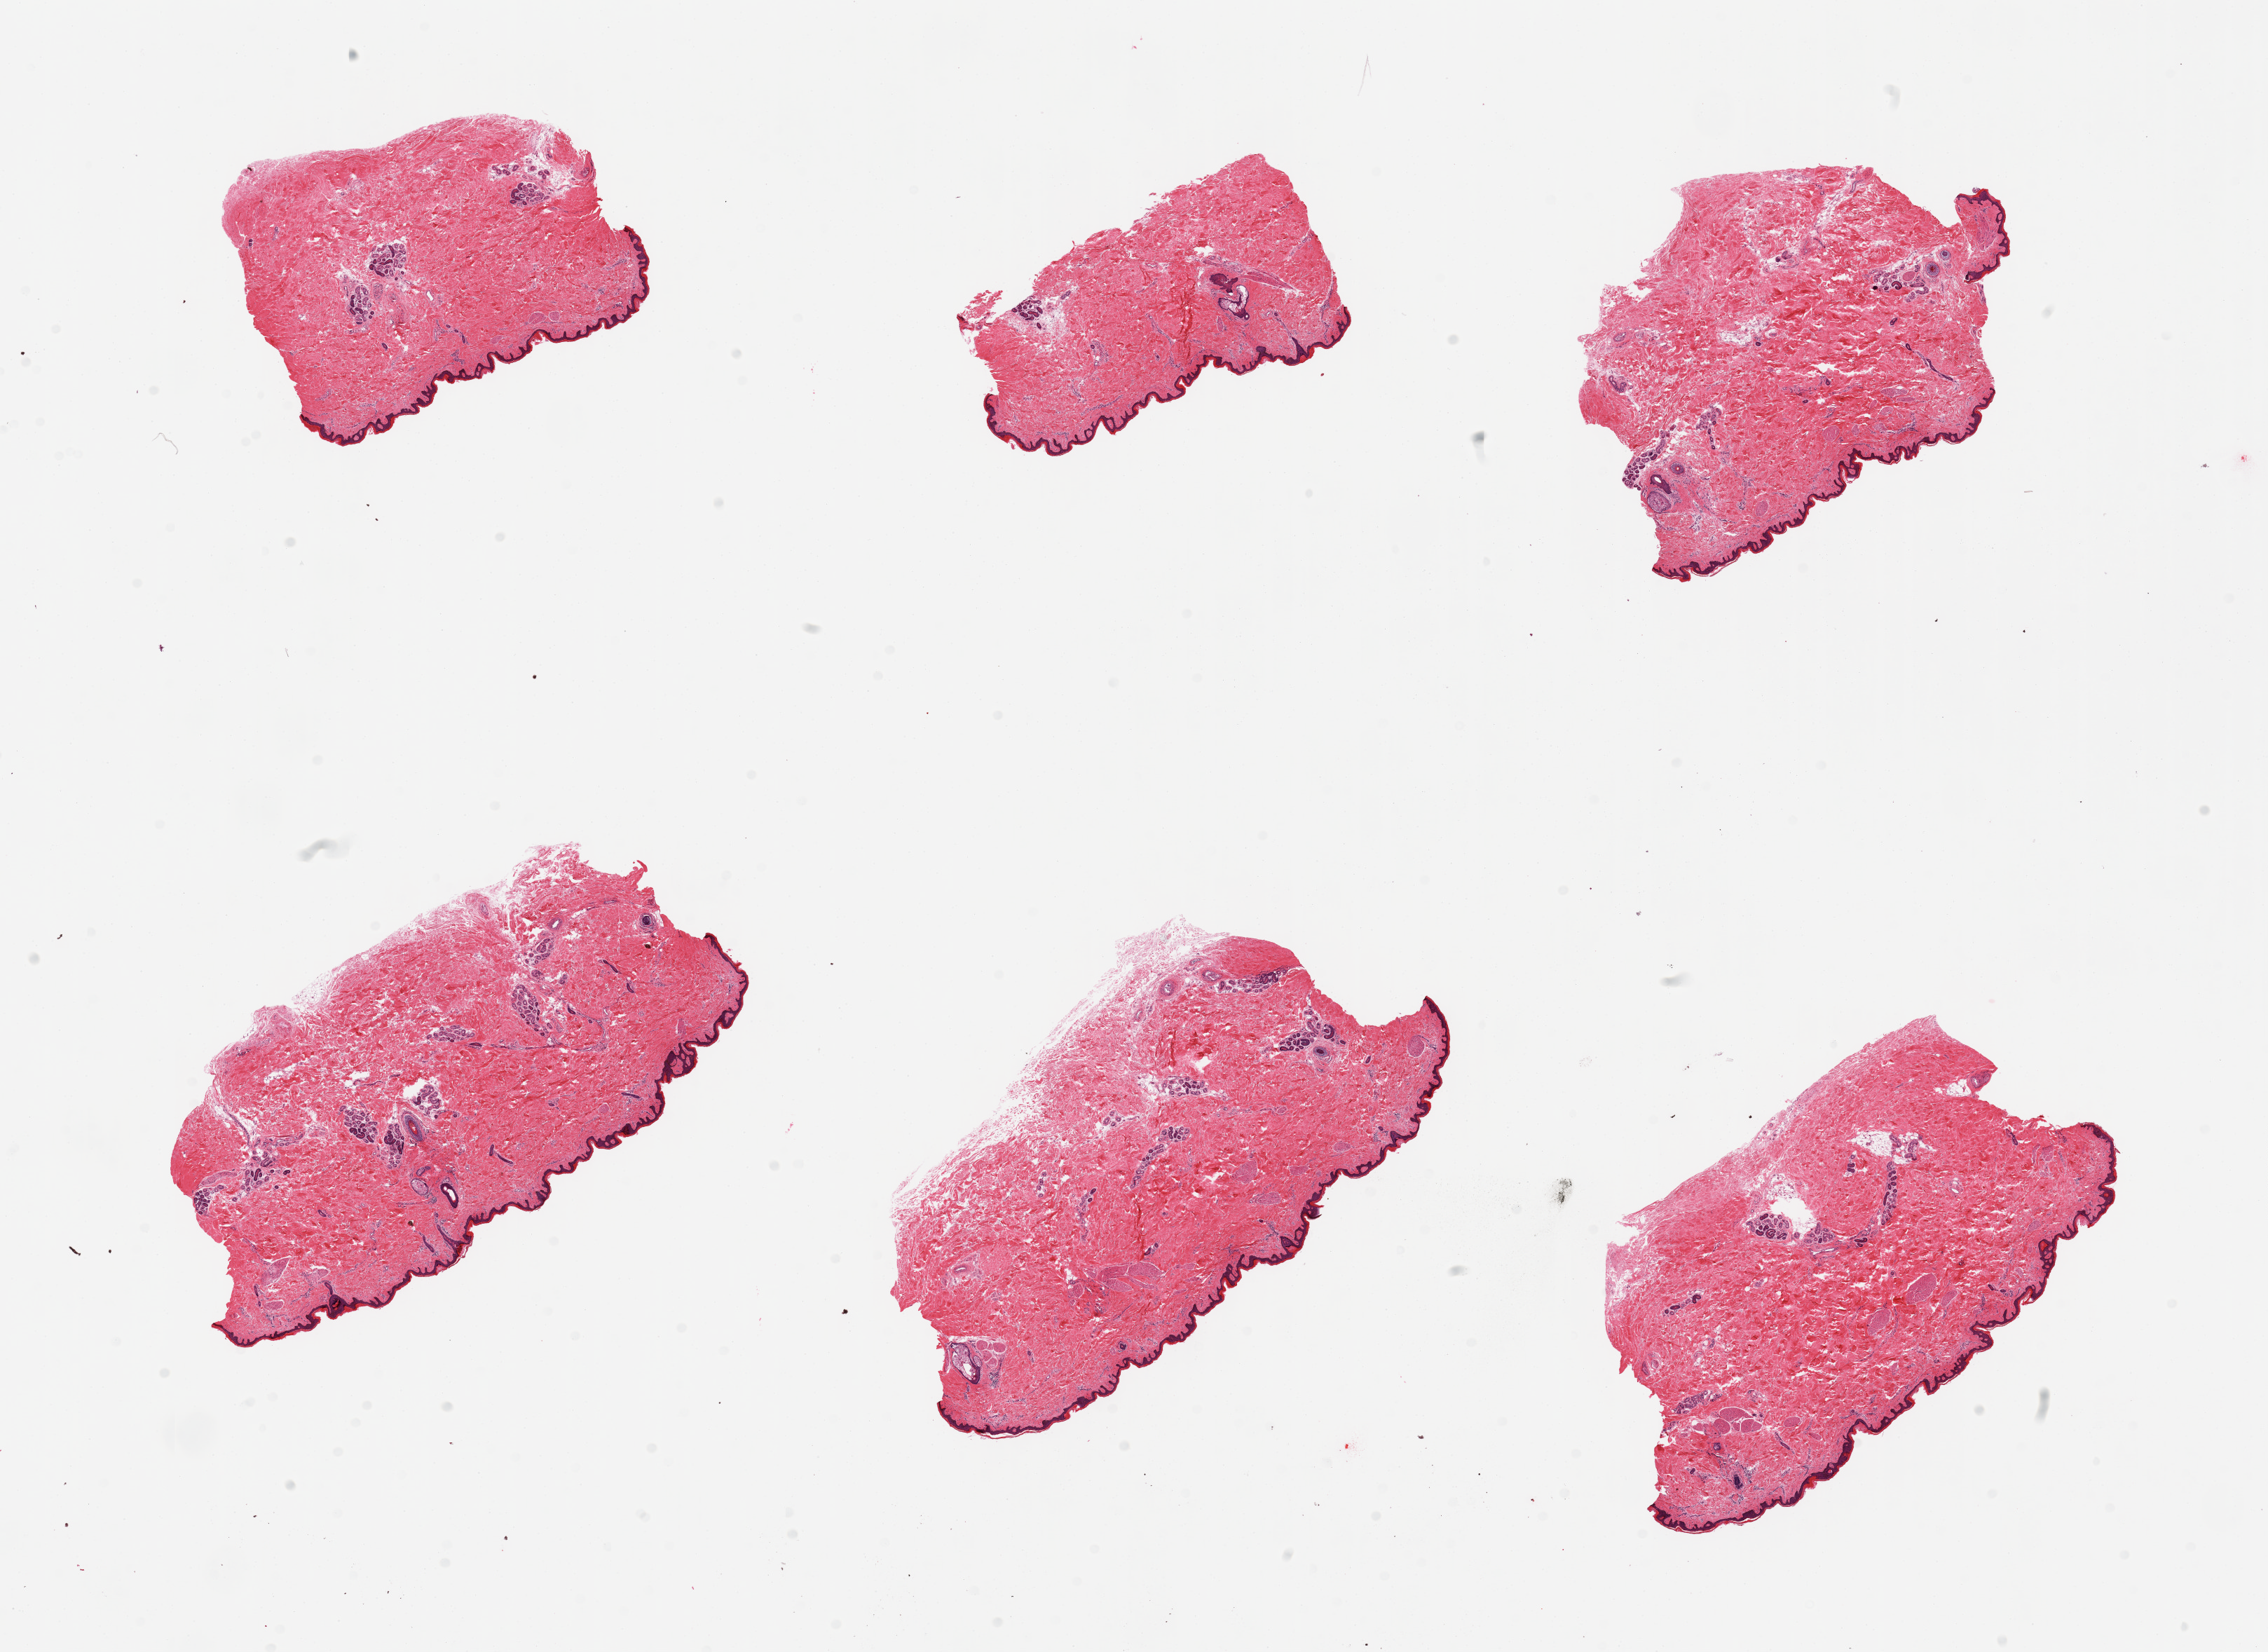
Digitized haematoxylin and eosin-stained section, brightfield — low-resolution overview of the scanned area, about 25.6 x 18.6 mm (from a 20x scan), PAXgene-fixed, paraffin-embedded tissue, target tissue: skin of lower leg, donor tissue sample. Donor sex: male.
- reviewer comment on this tissue sample: 6 pieces; well trimmed